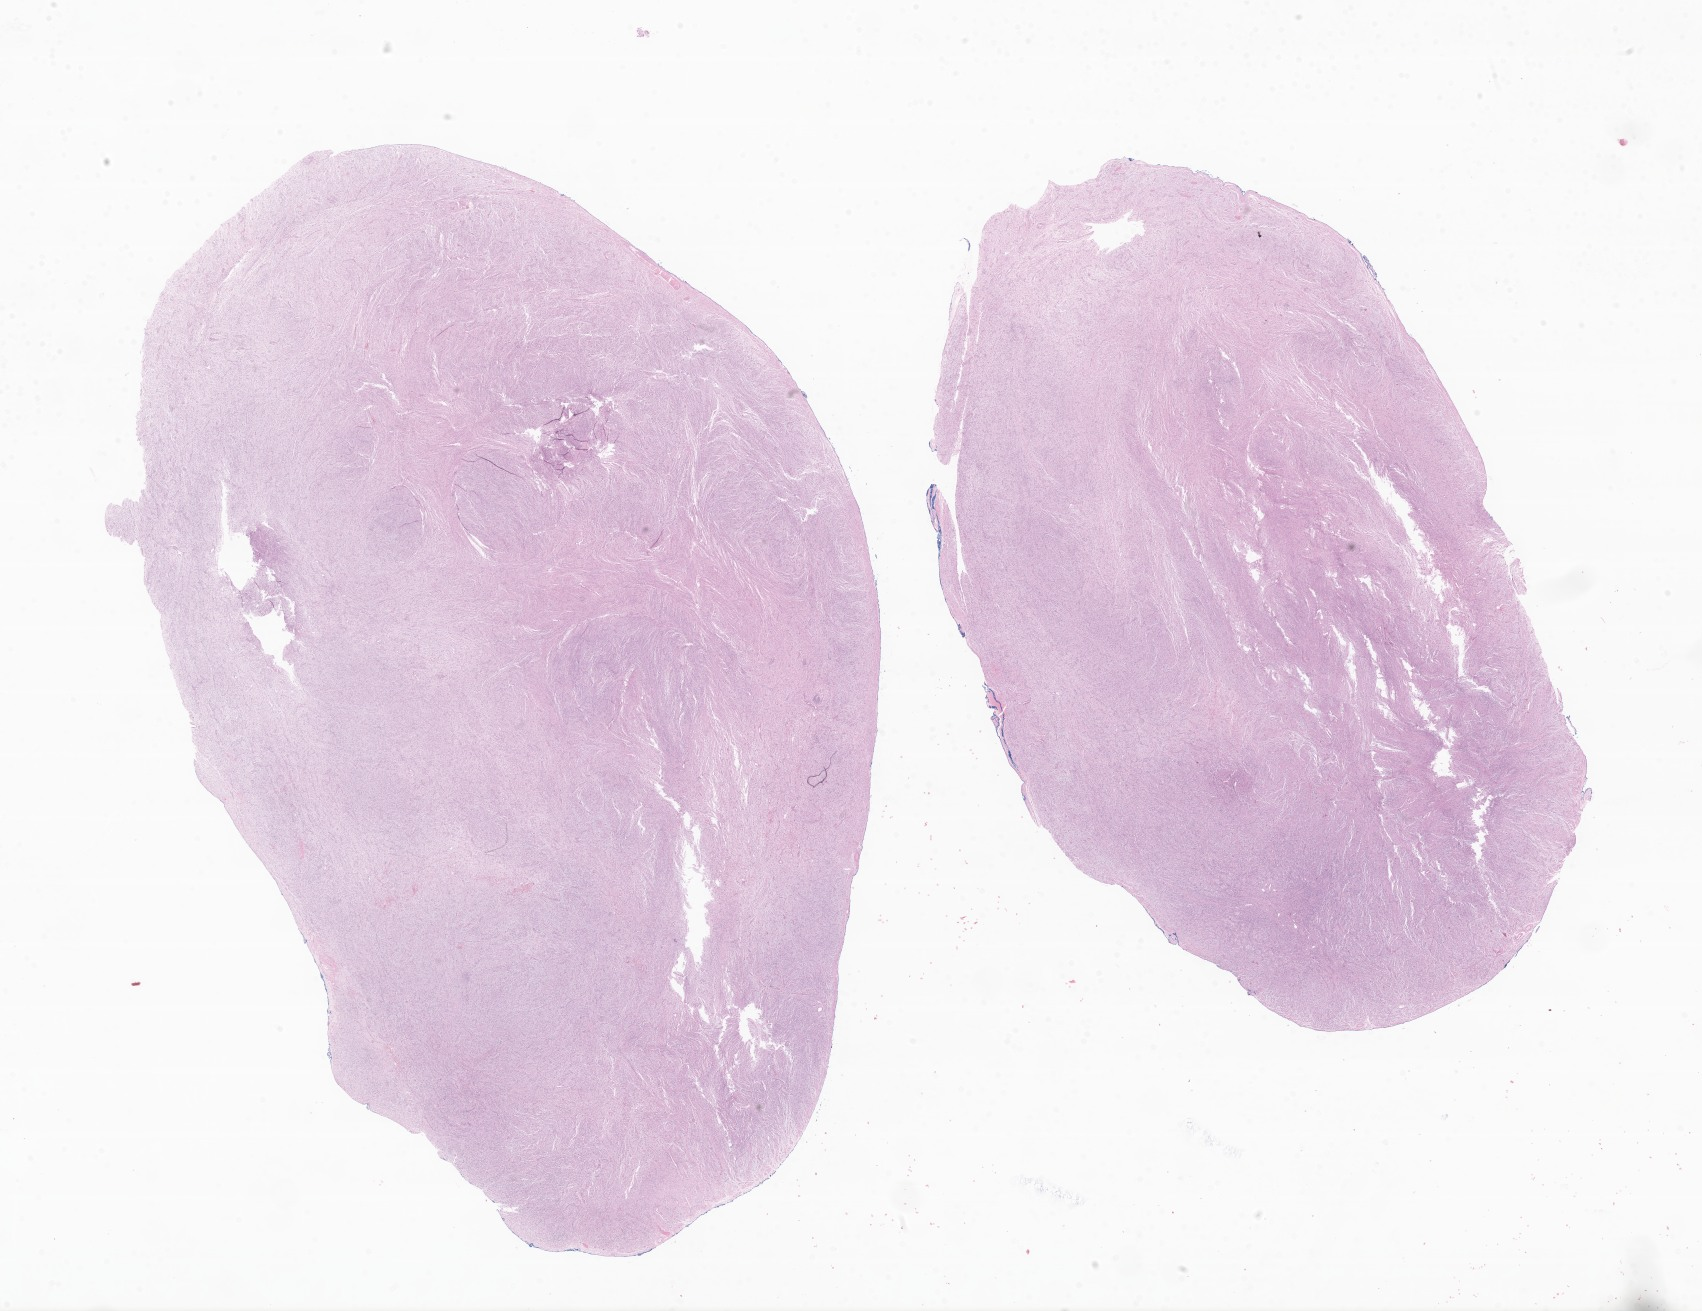
Digitized haematoxylin and eosin-stained section of tumor tissue from the head and neck — low-resolution overview of the scanned area, about 28.7 x 22.1 mm, FFPE section. Male patient, age 143 days.
• diagnosis (ICD-O-3 morphology term): Embryonal rhabdomyosarcoma, NOS